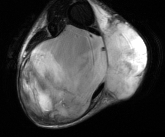
MRI of an extremity soft-tissue mass, one axial slice; position 32 of 81 along the scan axis; T2-weighted fat-saturated; MR volume resampled by the dataset authors to the PET/CT grid (not the native acquisition matrix); 3.27 mm slice thickness; 165 × 137 image matrix. Male patient. Case-level facts recorded for this patient, not image findings: histological type: liposarcoma - round cell; grade: high; site of the primary tumour: right calf.
Structures marked on this image (expert contour drawn on MRI and transferred to this co-registered scan by the dataset authors):
- gross tumour volume (mass): bounding box <21,23,147,120> (left, top, right, bottom; pixels)